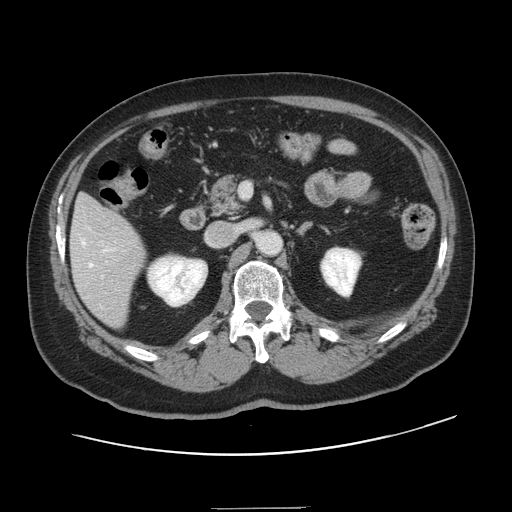
Contrast-enhanced abdominal CT, one axial slice. Position 67 of 143 along the scan axis. 120 kVp. Intravenous contrast given. Soft-tissue window (W 400 / L 40 HU). 512 × 512 image matrix. Male patient, age 62 years. Case-level facts recorded for this patient, not image findings: diagnosis: colorectal cancer liver metastases, imaged before liver resection; multiple liver metastases: yes; largest metastasis: 2.7 cm; disease in both lobes: no.
Outlined on this slice (manually delineated by an expert):
- hepatic veins: bounding box <82,240,109,268> (left, top, right, bottom; pixels)
- liver: <71,196,145,328>
- planned liver remnant (the part of the liver to remain after resection): <76,196,103,216>
- portal vein (with intrahepatic branches): <101,241,107,263>